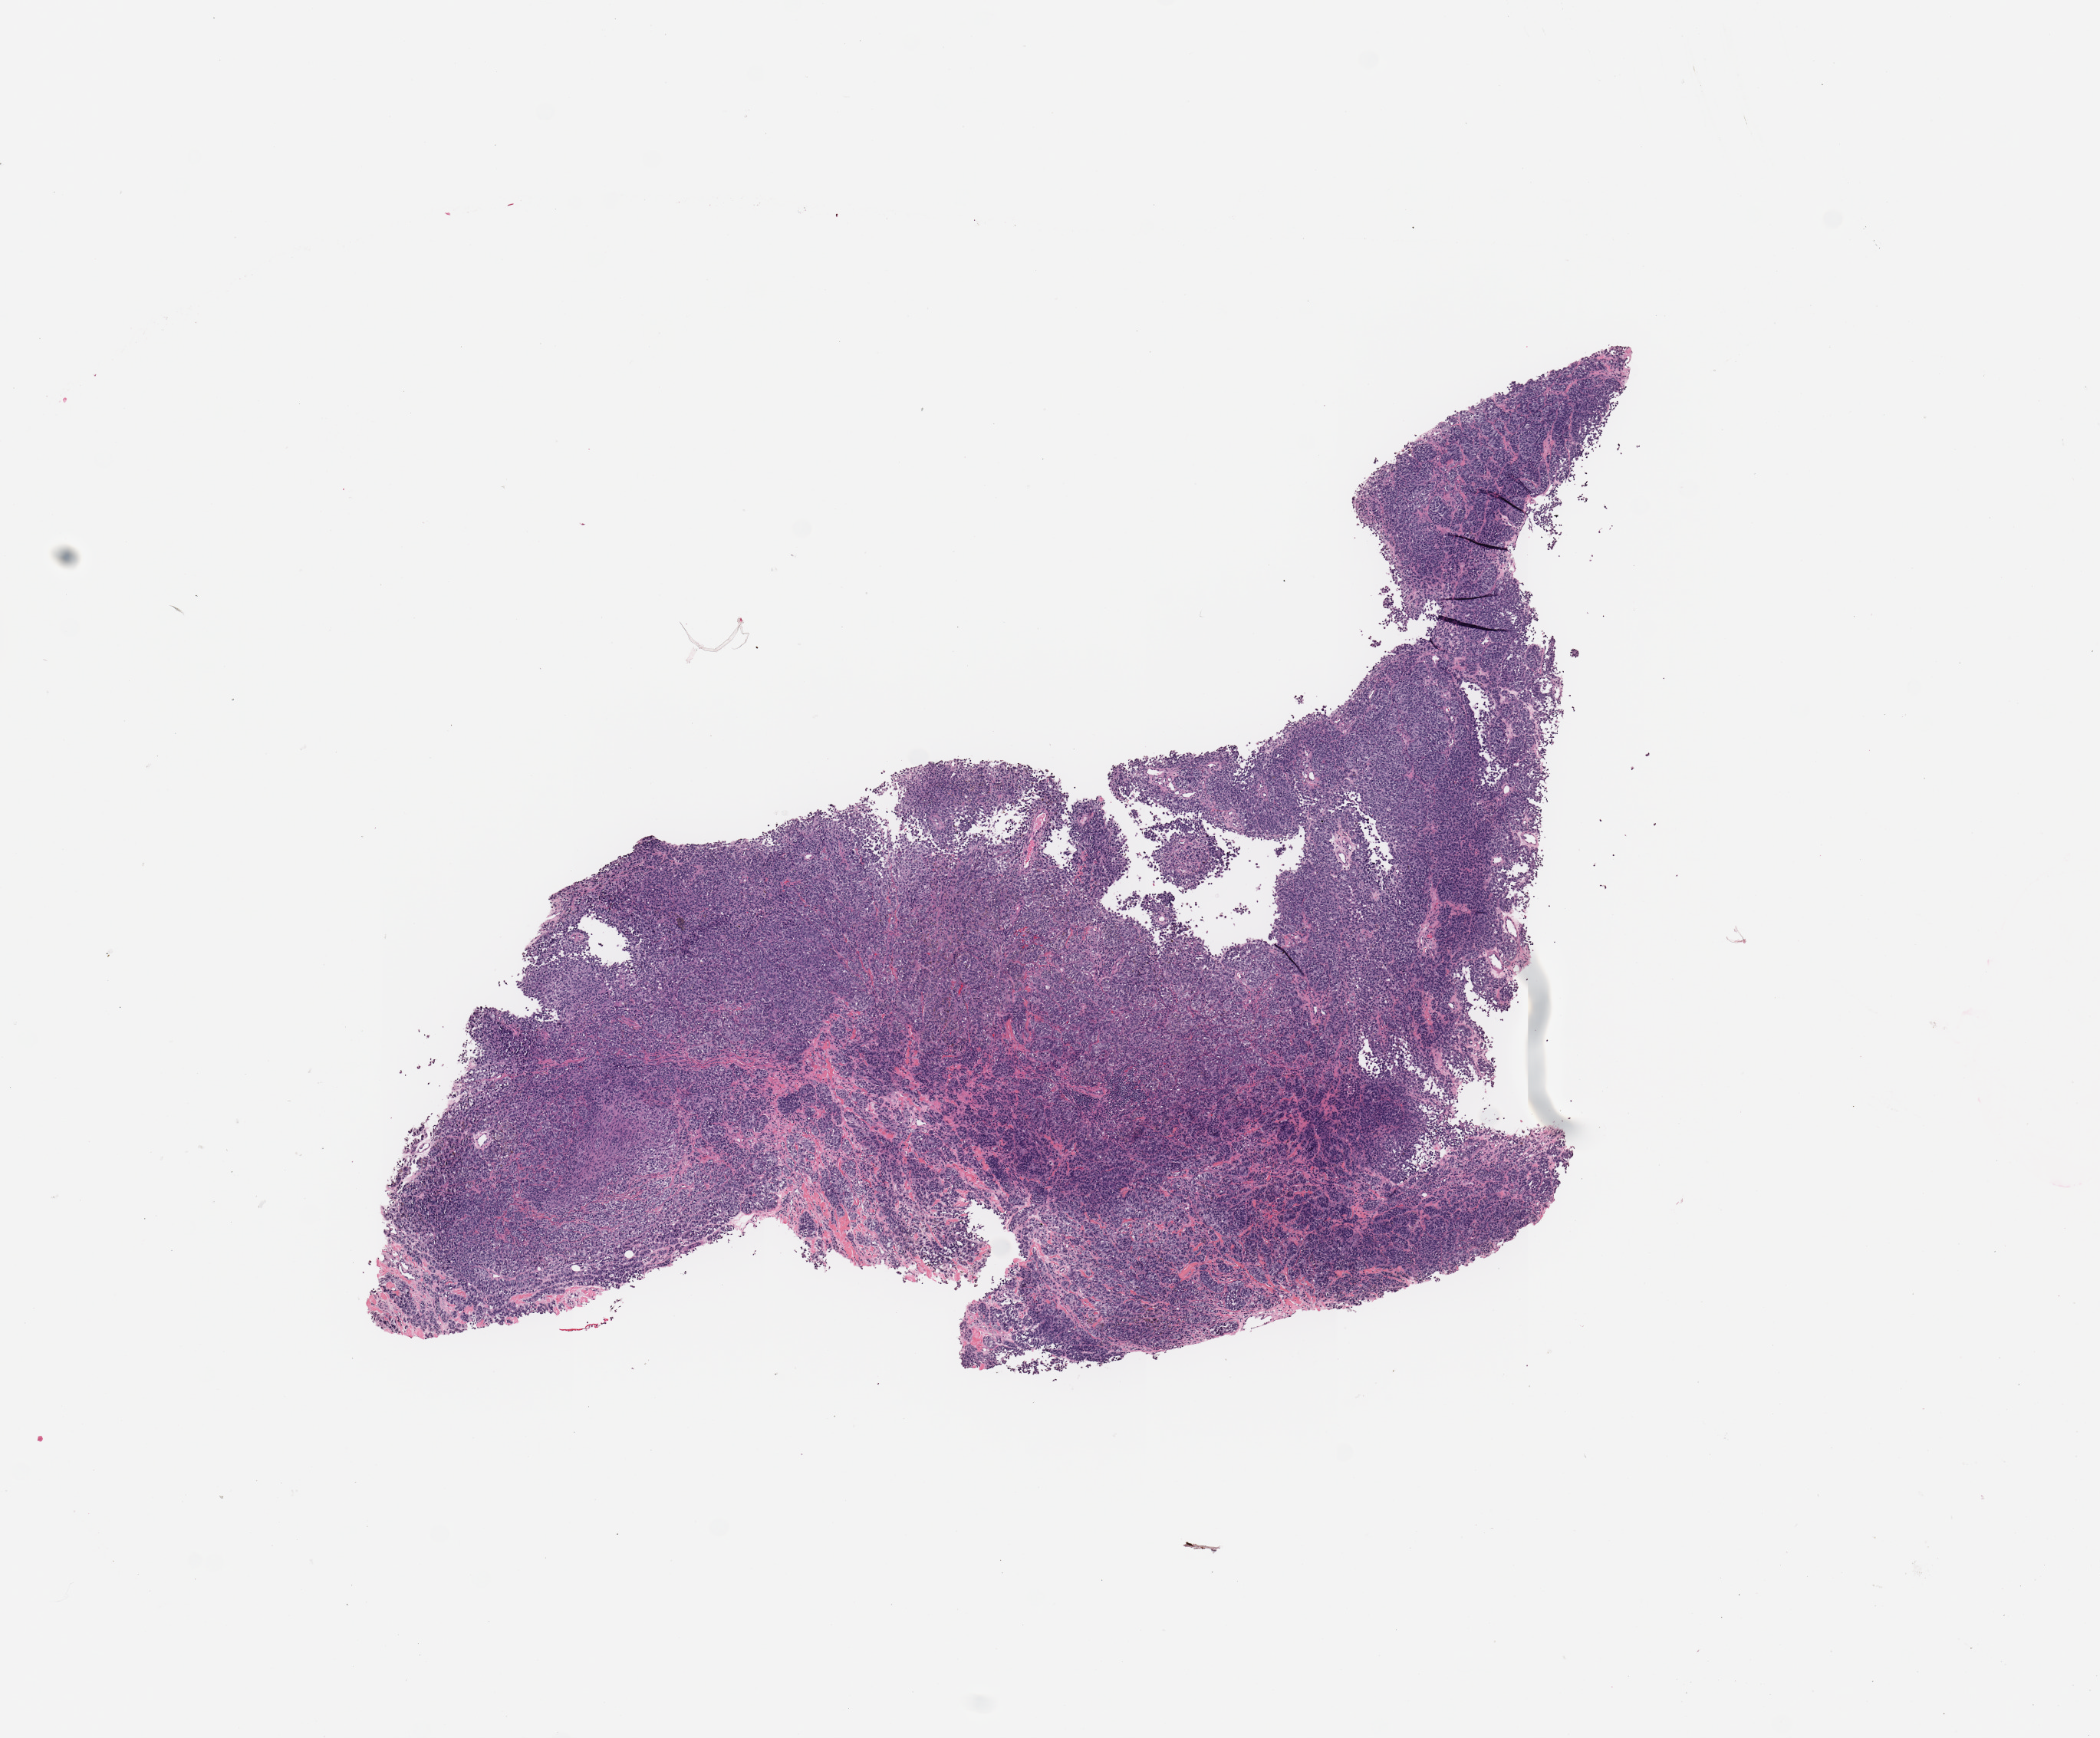
H&E whole-slide image, low-resolution overview of the scanned area, about 10.8 x 9.0 mm (slide scanned at 20x); tumour tissue sample, sampled site: skin. 73-year-old female patient. Pathologist review of this section (percent, as recorded): tumour nuclei 90%, necrosis 0%.
Diagnosis: Malignant melanoma, NOS.